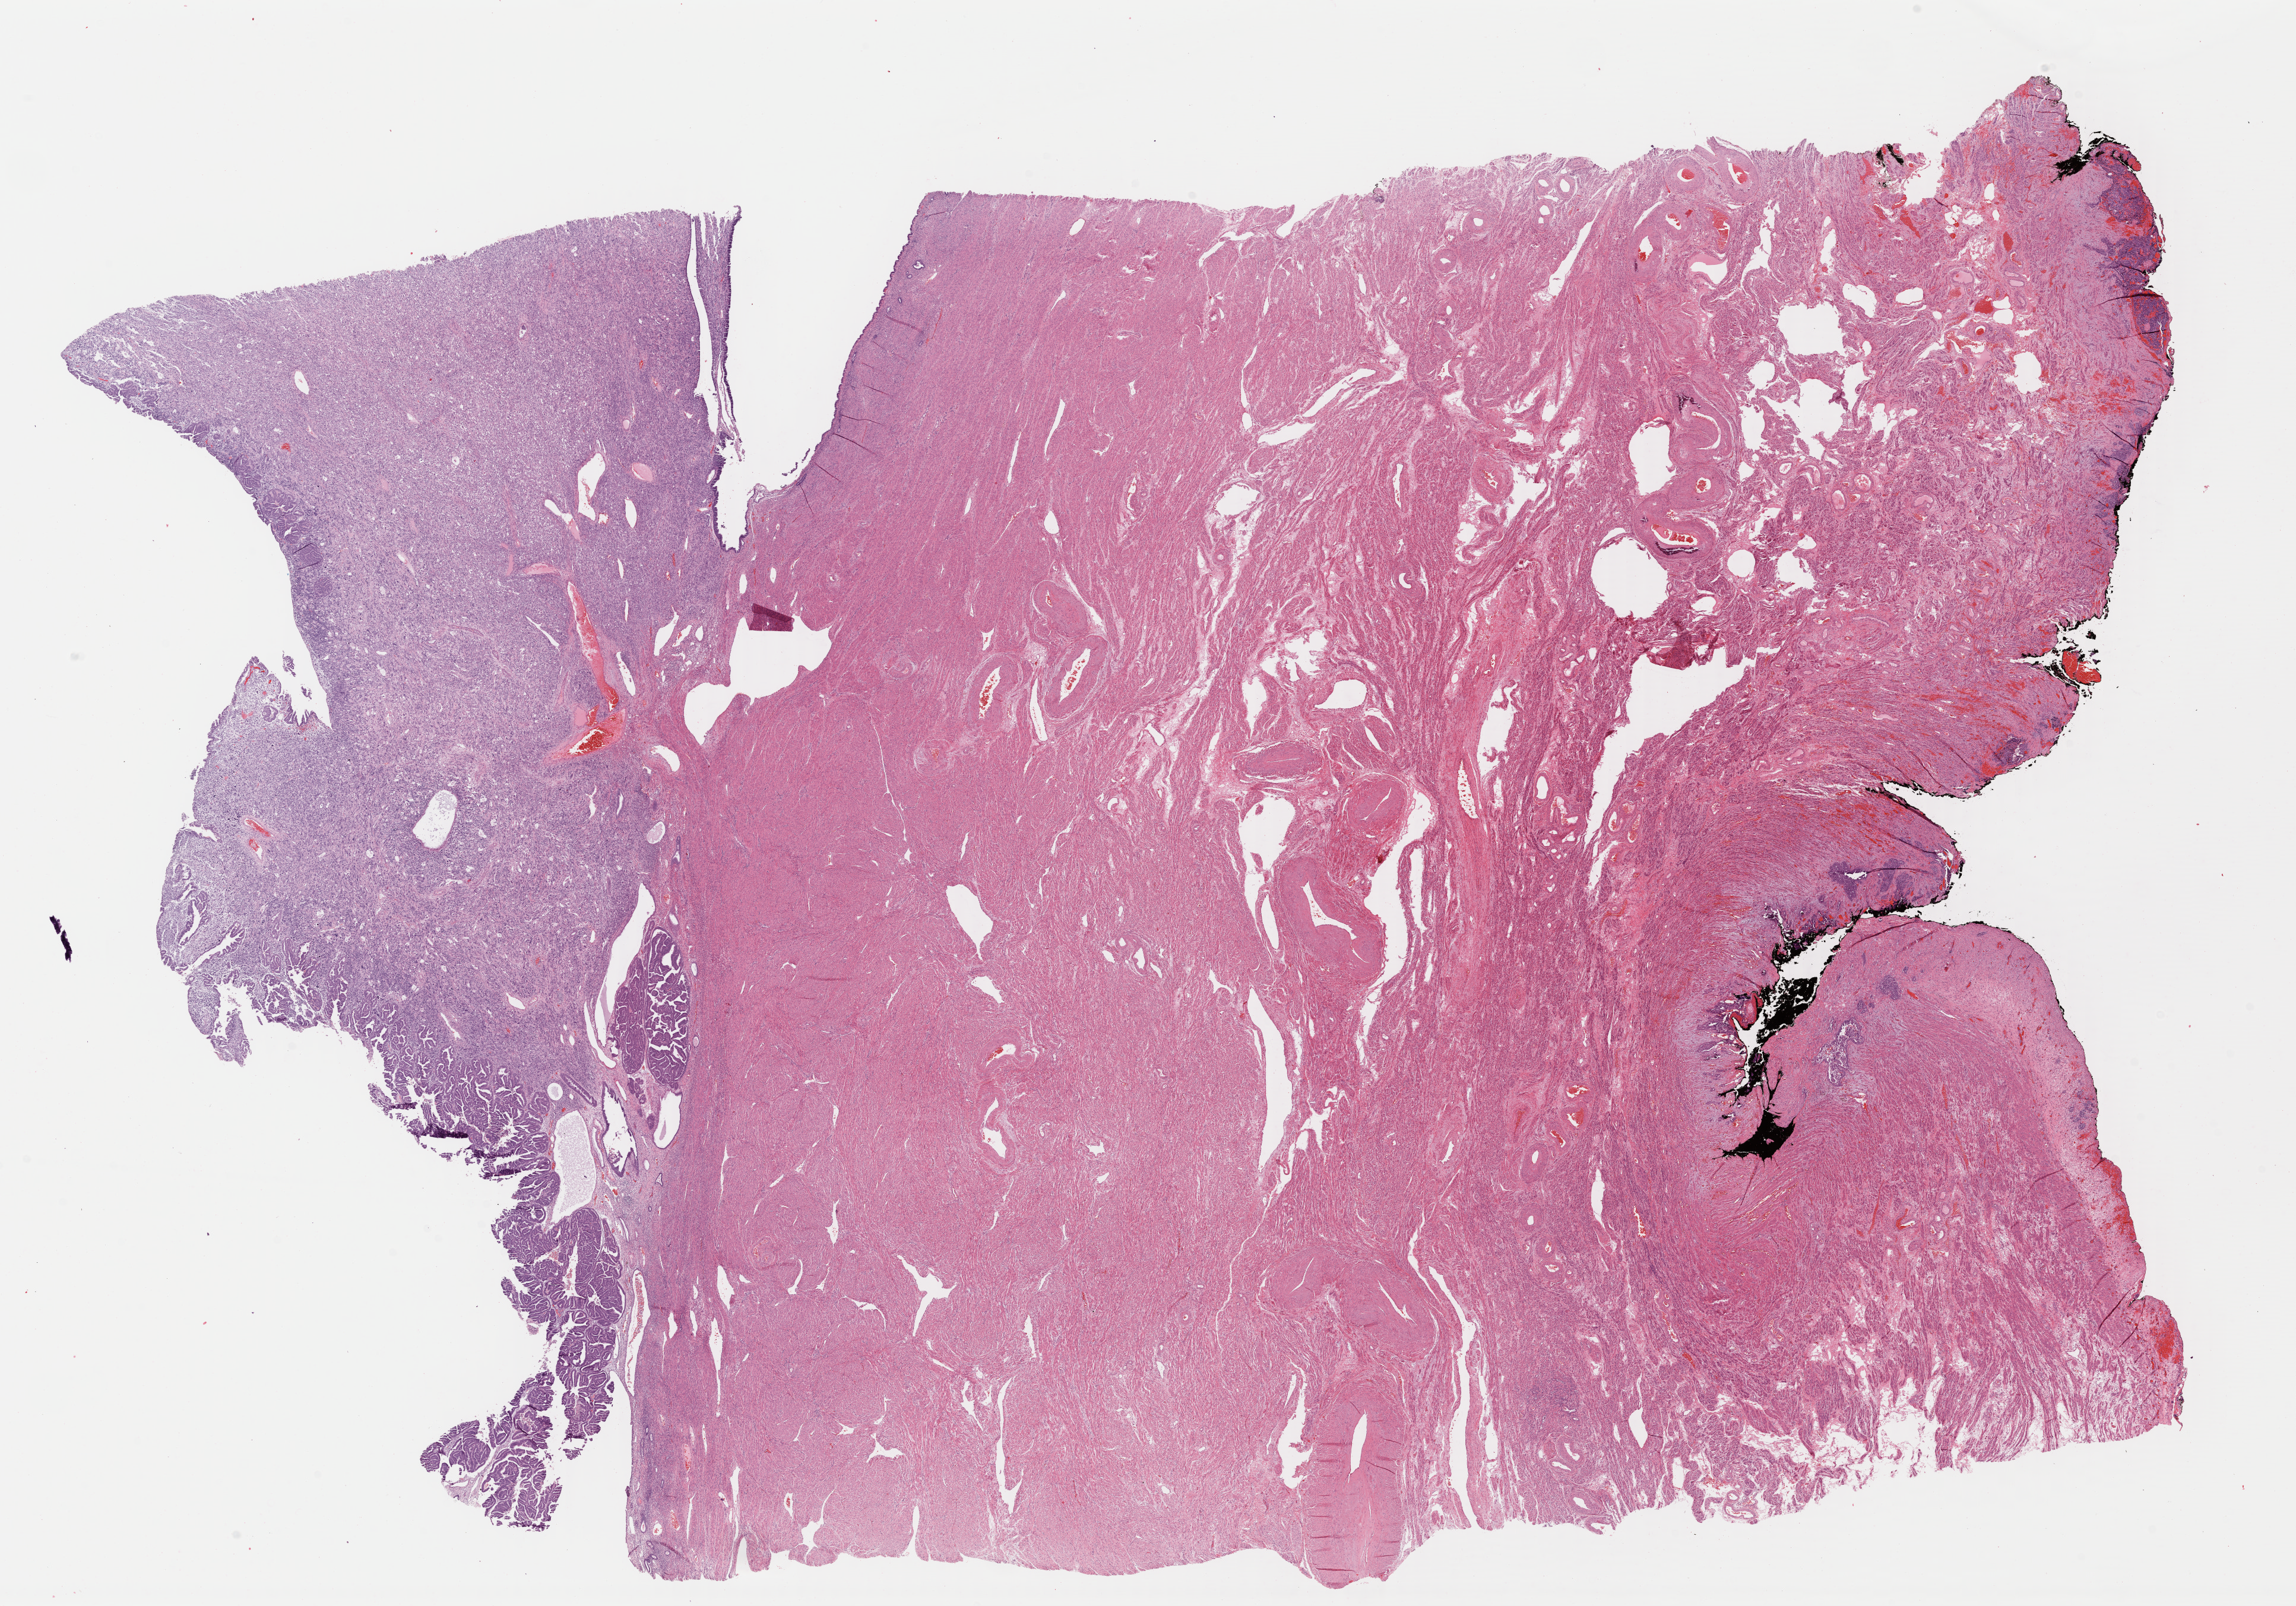
H&E whole-slide image — low-resolution overview of the scanned area, about 30.4 x 21.3 mm. FFPE section. Uterus, primary tumour sample. Female patient; age at initial diagnosis 63 years.
* pathologic diagnosis: Mullerian mixed tumor (endometrium)
* FIGO stage: IIIB